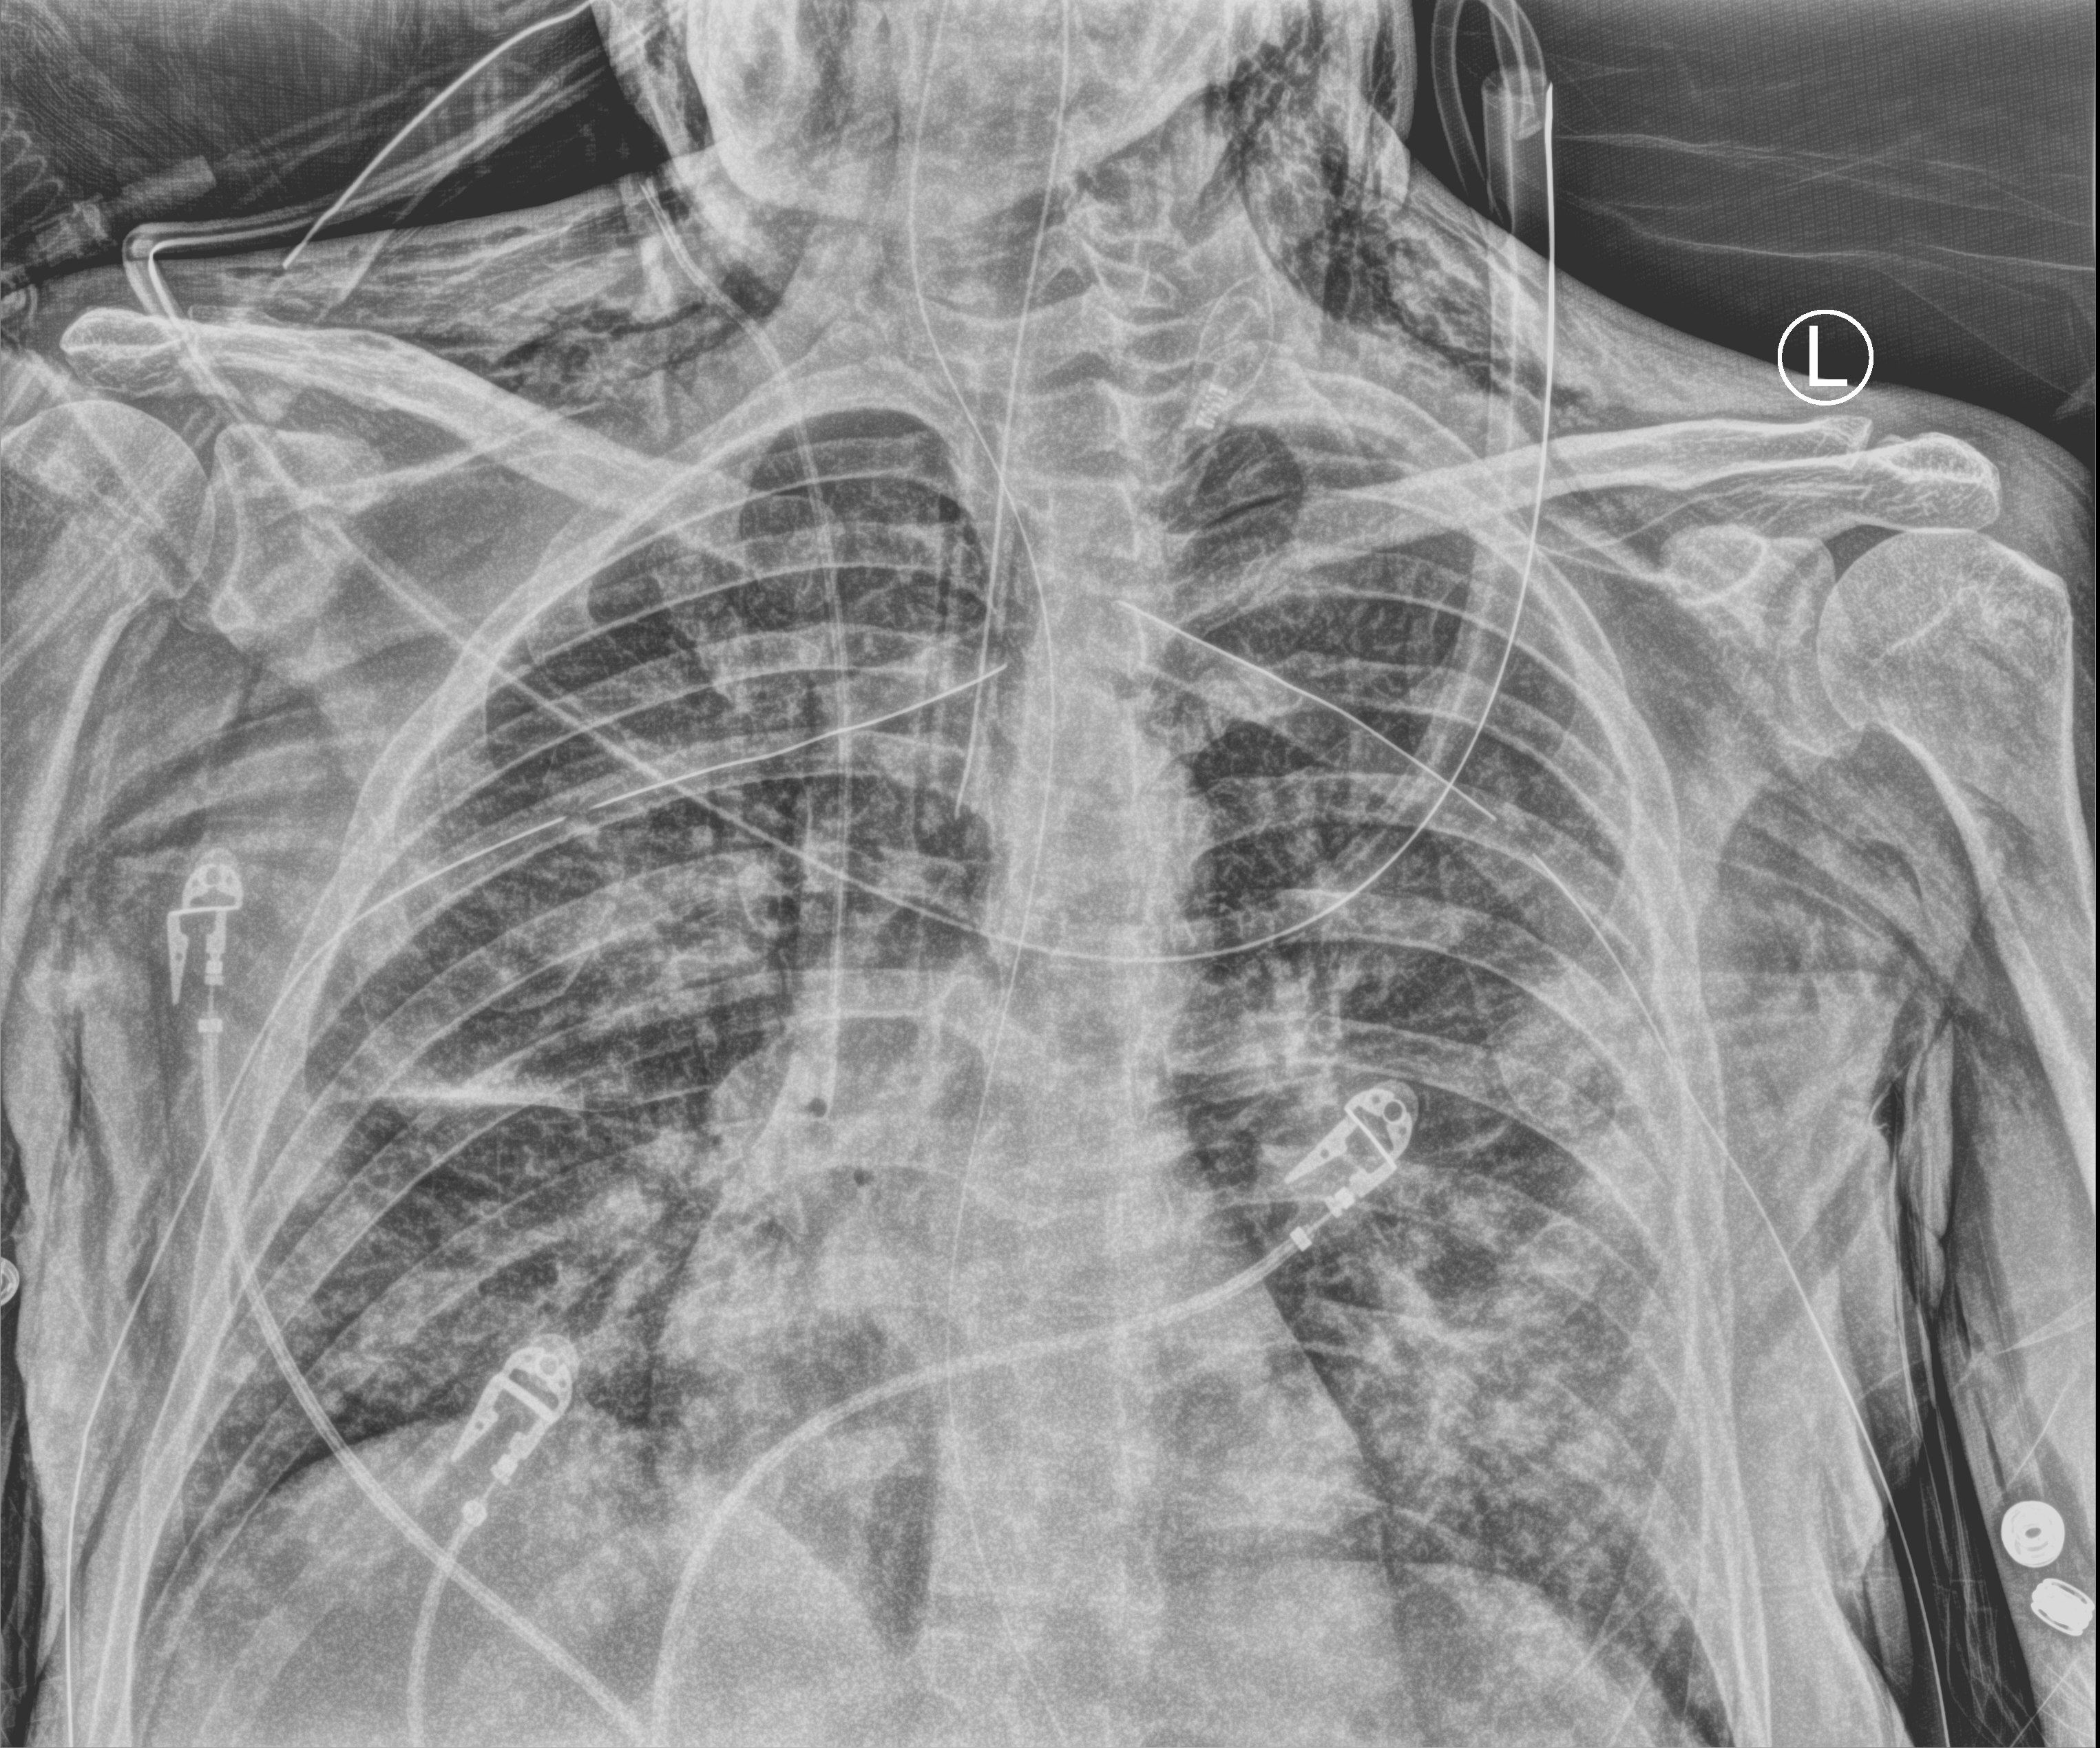
Portable chest radiograph. Patient hospitalised with COVID-19; male, aged 18–59 years.
Admission-level facts for this patient (not findings on this image; timing relative to this image not recorded): admitted to intensive care during this hospital stay: yes.